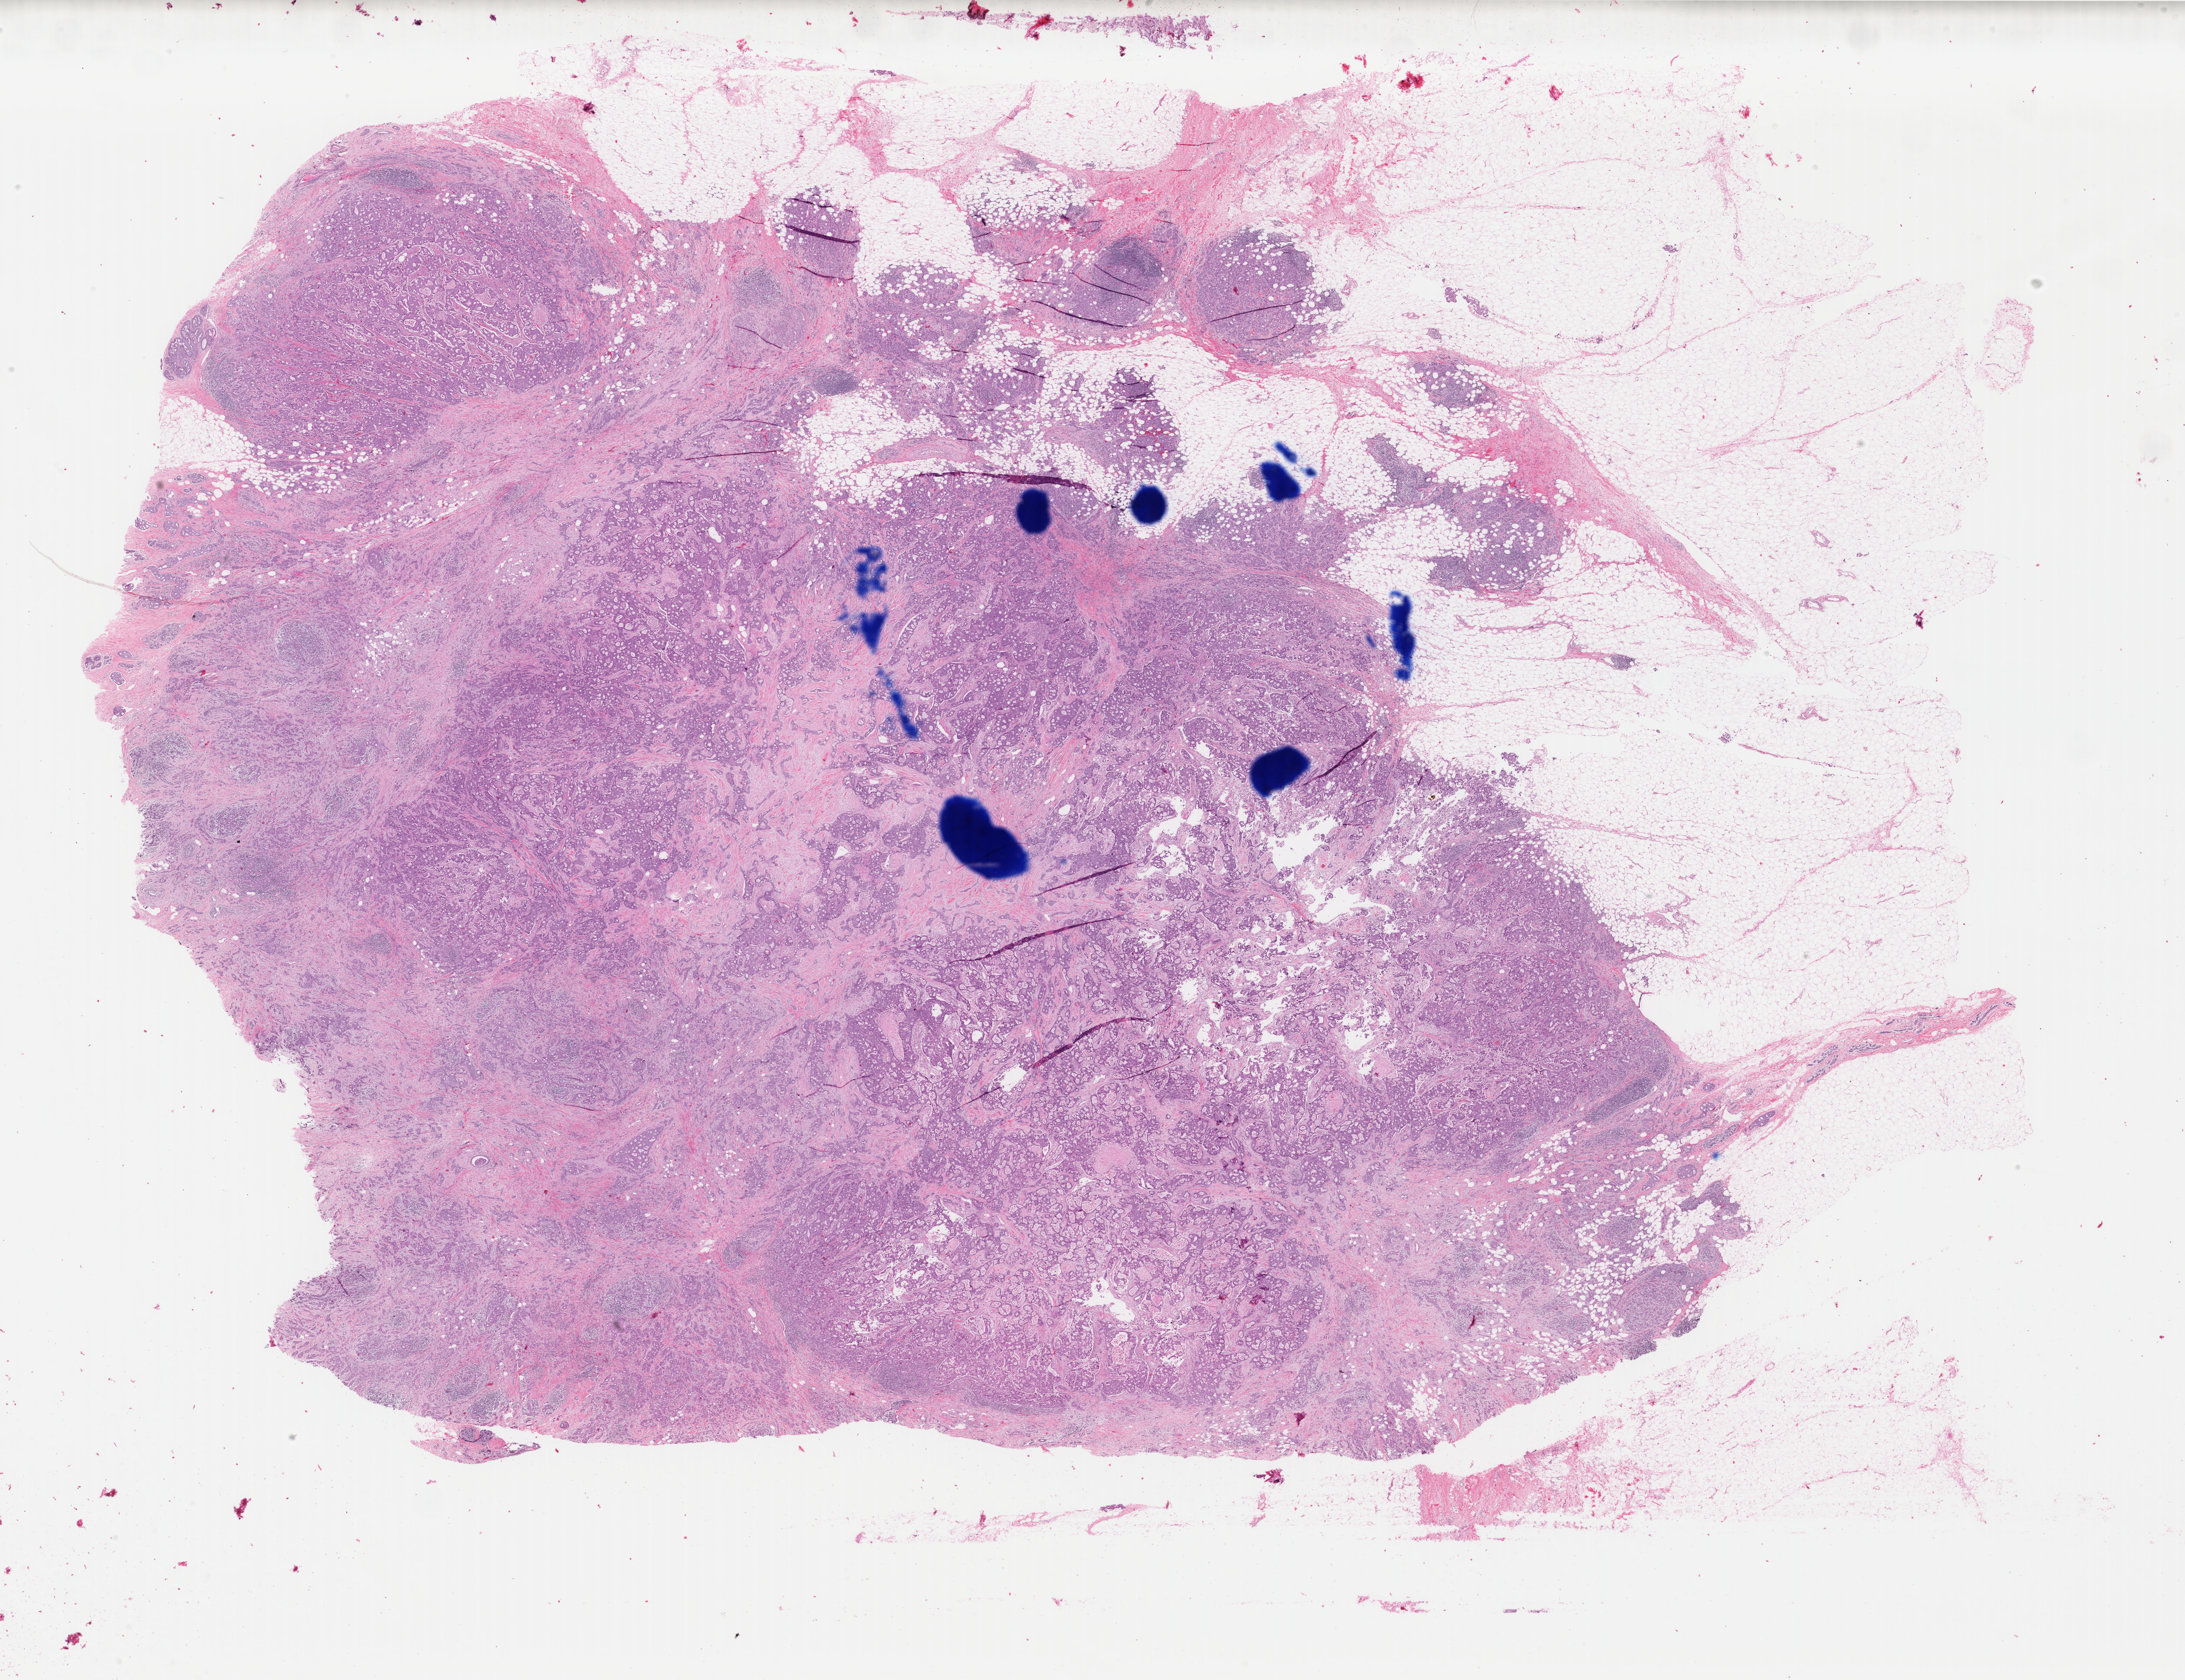
Digitized Hematoxylin and eosin (H&E) stained tissue section (whole slide) — low-resolution overview of the scanned area, about 29.7 x 22.9 mm (from a 40x scan). FFPE section. Sample: primary tumour, breast. Female, age 51 years at initial diagnosis.
Pathologic diagnosis: Infiltrating duct carcinoma, NOS. Laterality: left. AJCC pathologic stage: IIA.